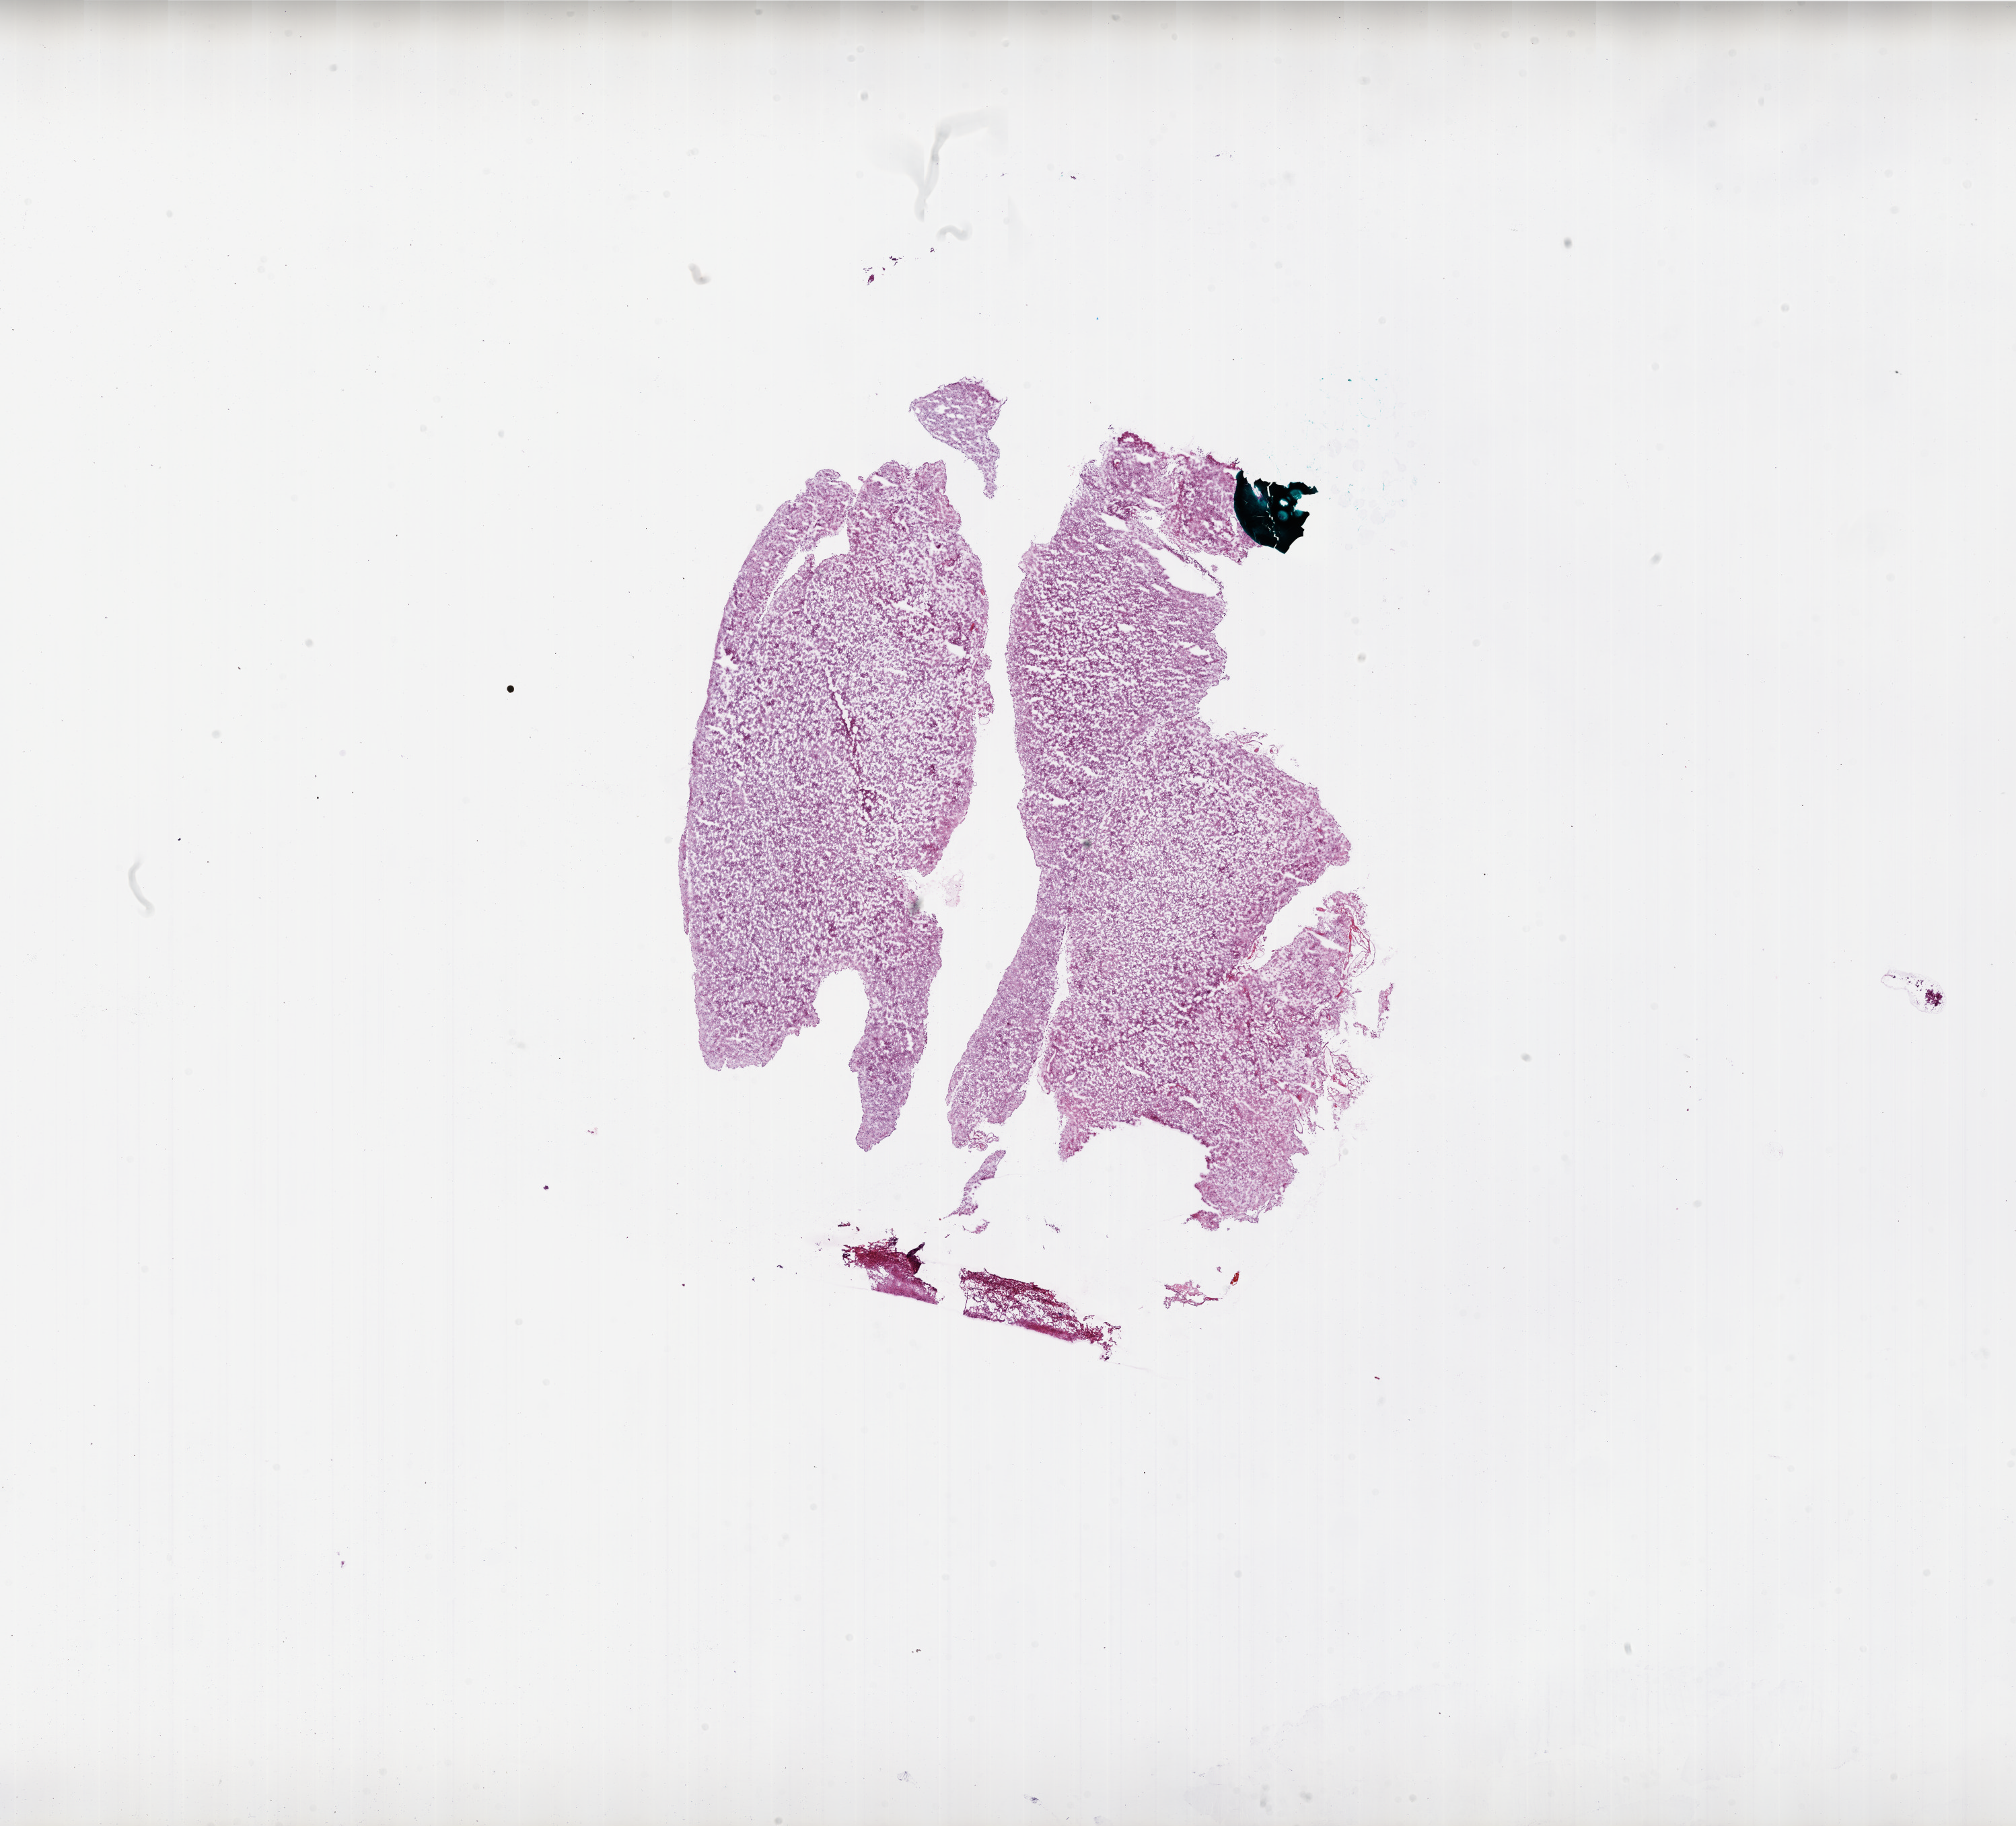
H&E-stained whole-slide image, shown as a low-resolution overview of the whole scanned area (about 24.0 x 21.7 mm, from a 20x scan). Frozen section from the bottom of the tissue portion. Sample: primary tumour, brain. Female, age 69 years at initial diagnosis. Slide review estimates, as recorded: tumour cells 70%, tumour nuclei 80%, normal cells 0%, stromal cells 30%, necrosis 0%.
Histologic diagnosis: Glioblastoma.